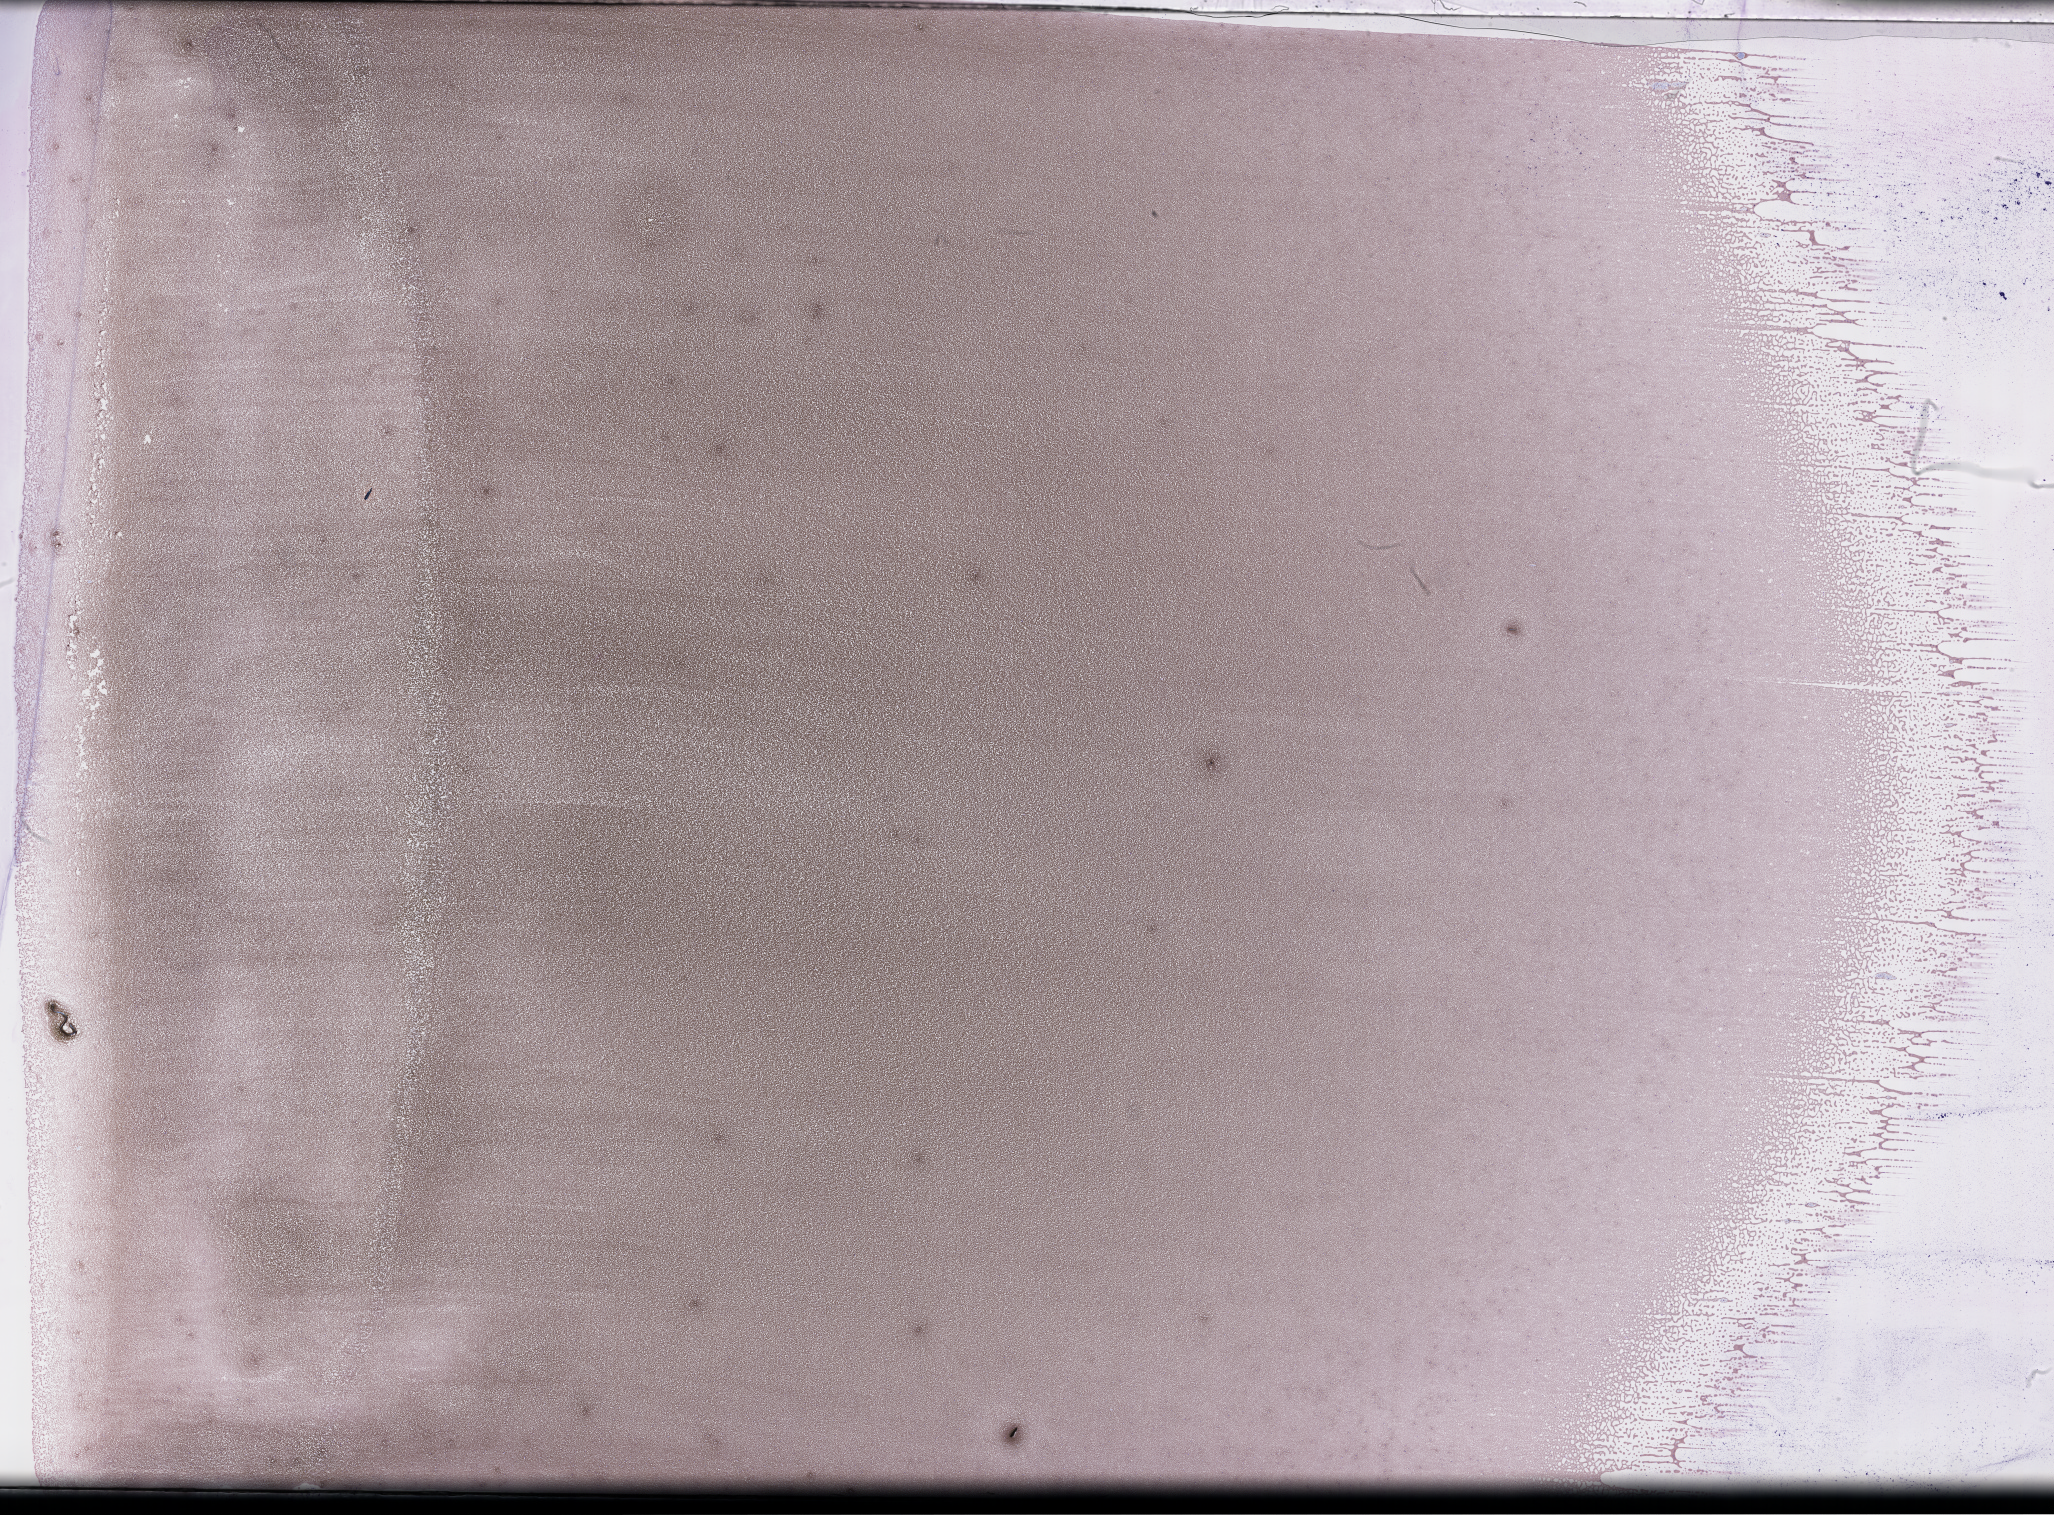
Whole-slide image of a whole blood smear, Wright-Giemsa stain — a low-resolution overview of the entire scanned area, about 33.2 x 24.5 mm; EDTA-anticoagulated smear; collected on treatment. Patient: male.
* patient diagnosis: Plasma Cell Myeloma